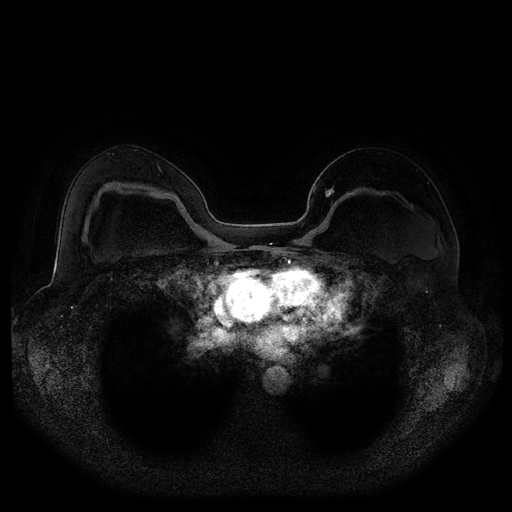
Breast MRI (dynamic contrast-enhanced, multi-phase), one axial slice. Position 67 of 116 along the scan axis. Dynamic contrast-enhanced series, time point 2 of 5 at this slice position (early post-contrast). 1.5 T. TE 2.5 ms, TR 5.2 ms. 2.1 mm slice thickness. 512 × 512 image matrix, field of view 380 × 380 mm. Patient: female, 43 years.
Annotated regions visible in this slice (semi-automatic segmentation, software-assisted and operator-edited):
- breast lesion (labelled benign in the annotation): bounding box <325,185,335,199> (left, top, right, bottom; pixels)